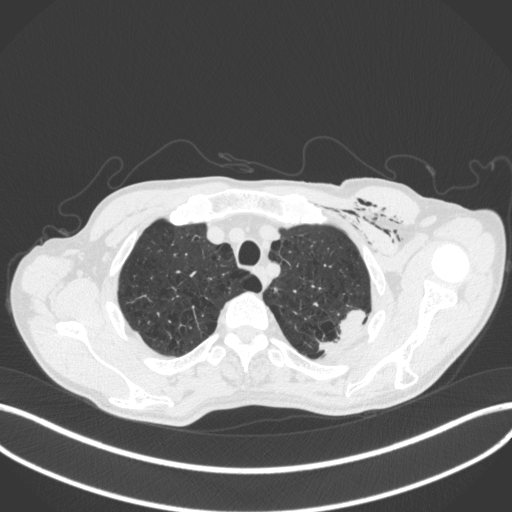
Chest CT, one axial slice. Position 352 of 416 along the scan axis. Reconstruction kernel B31f. 120 kVp. Lung window (W 1500 / L -600 HU). 1 mm slice thickness. 512 × 512 image matrix, field of view 400 × 400 mm. Male patient, age 58 years. Case-level facts recorded for this patient, not image findings: clinical TNM (as recorded): T3 N0 M0.
Annotated regions visible in this slice (rectangle marked by the reading radiologist):
- lung tumour (recorded histology: adenocarcinoma): box from (x=311, y=303) to (x=379, y=357) px